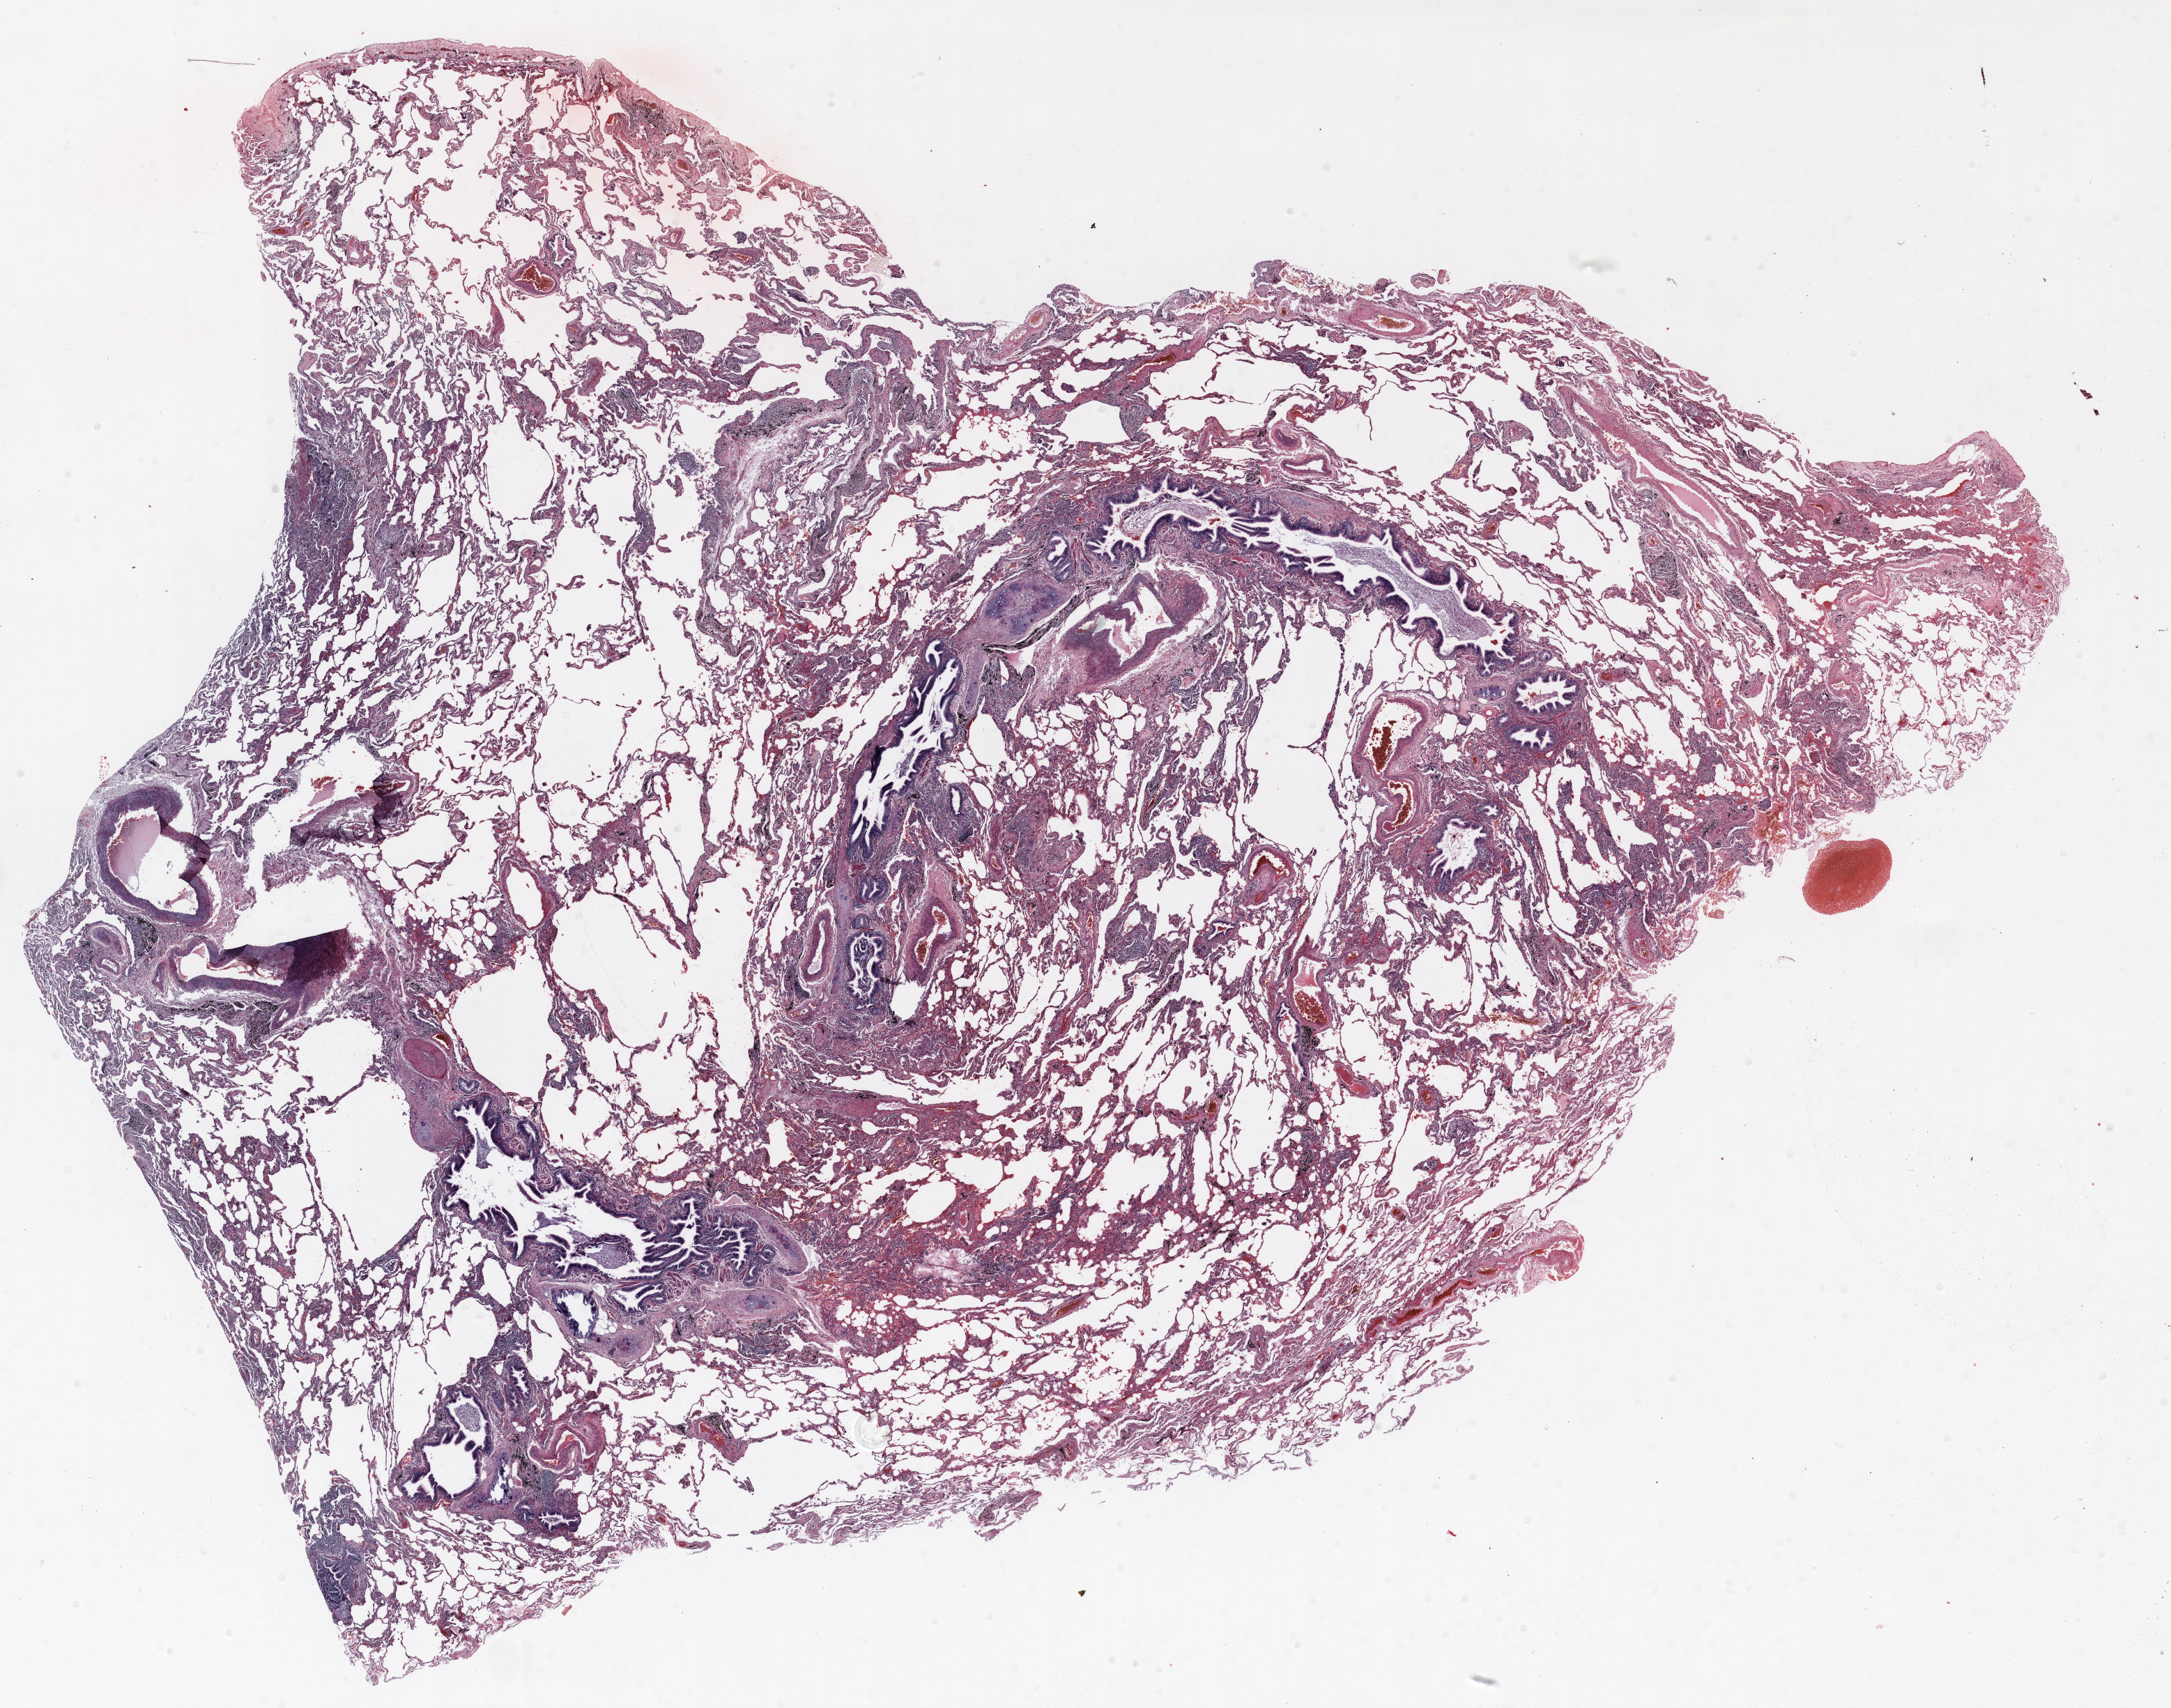
H&E-stained whole-slide image, low-resolution overview of the scanned area, about 25.0 x 19.7 mm (acquisition: 20x scan); FFPE section; lung. Female, age 68 at enrolment. Current smoker at enrolment. Grade: undifferentiated (G4).
* participant's lung-cancer diagnosis: Large cell carcinoma, NOS
* primary tumour location (clinical record): left upper lobe
* stage (AJCC 6th edition): IA
* tumour size (pathology): 10 mm